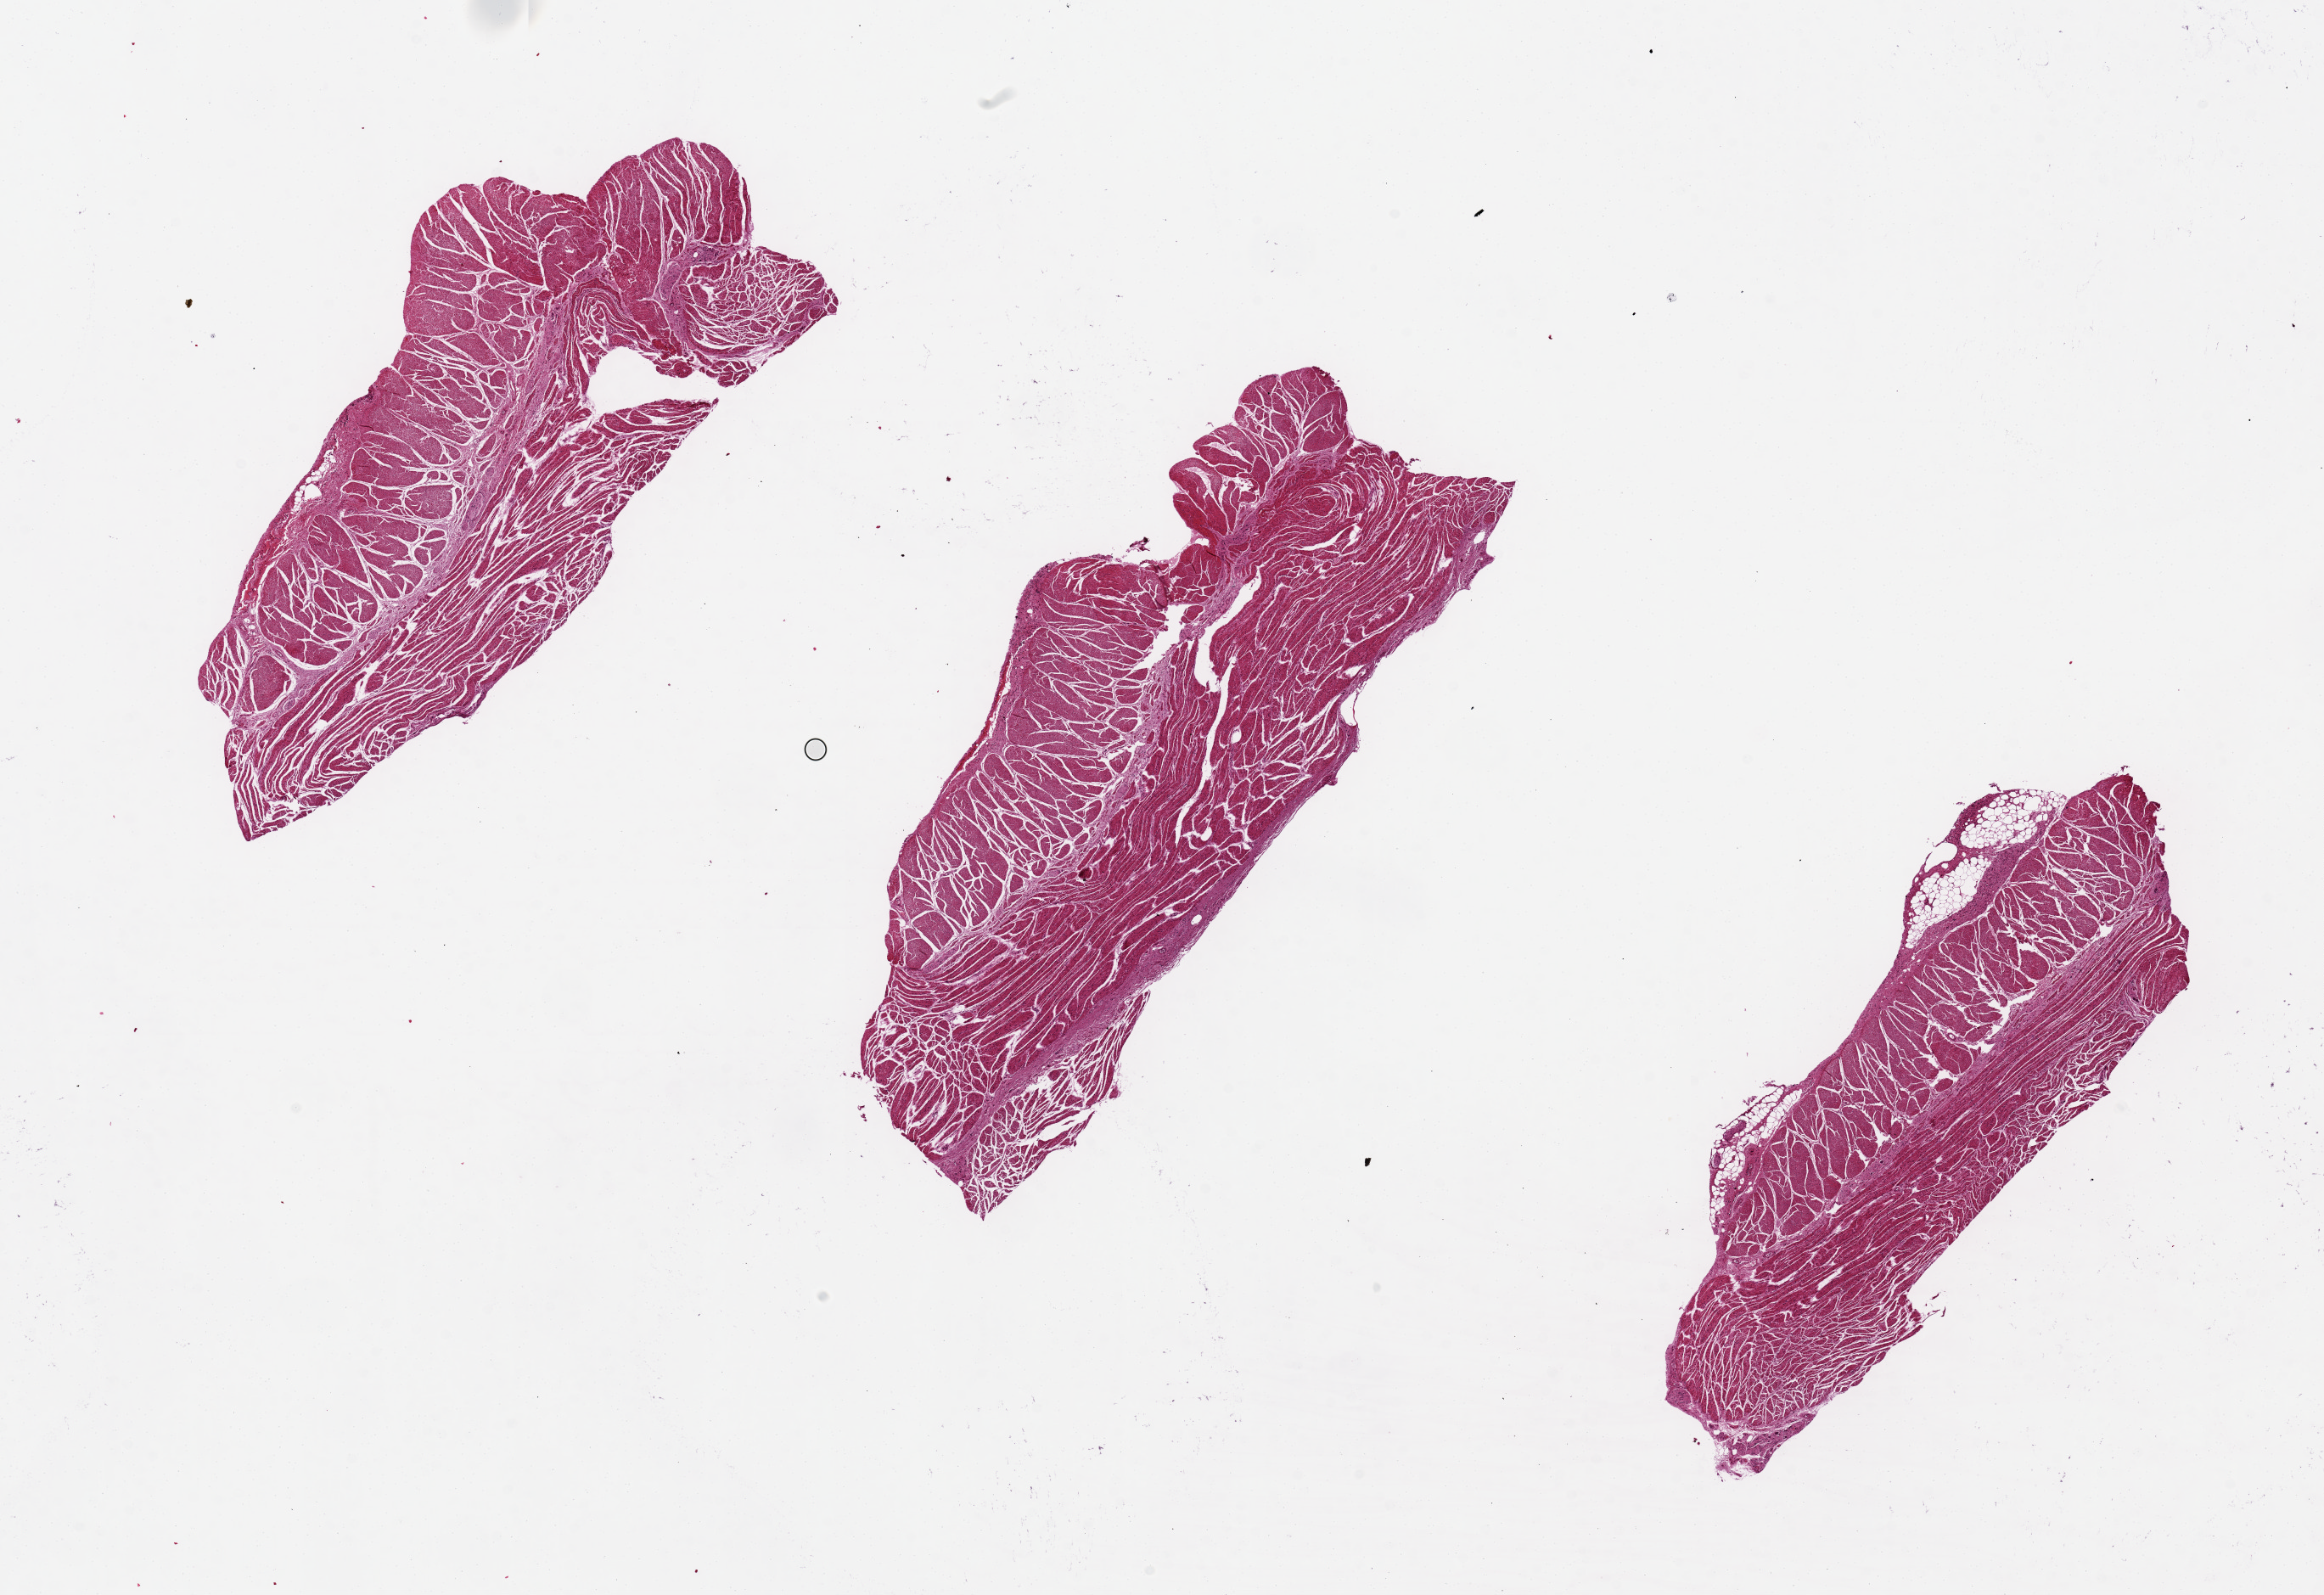
Digitized H&E-stained section, a low-resolution overview of the entire scanned area, about 21.7 x 14.9 mm (acquisition: 20x scan), PAXgene-fixed, paraffin-embedded tissue, target tissue: esophageal muscle, tissue donor sample. Male donor.
Review note (as recorded): 7.9x3.2mm.